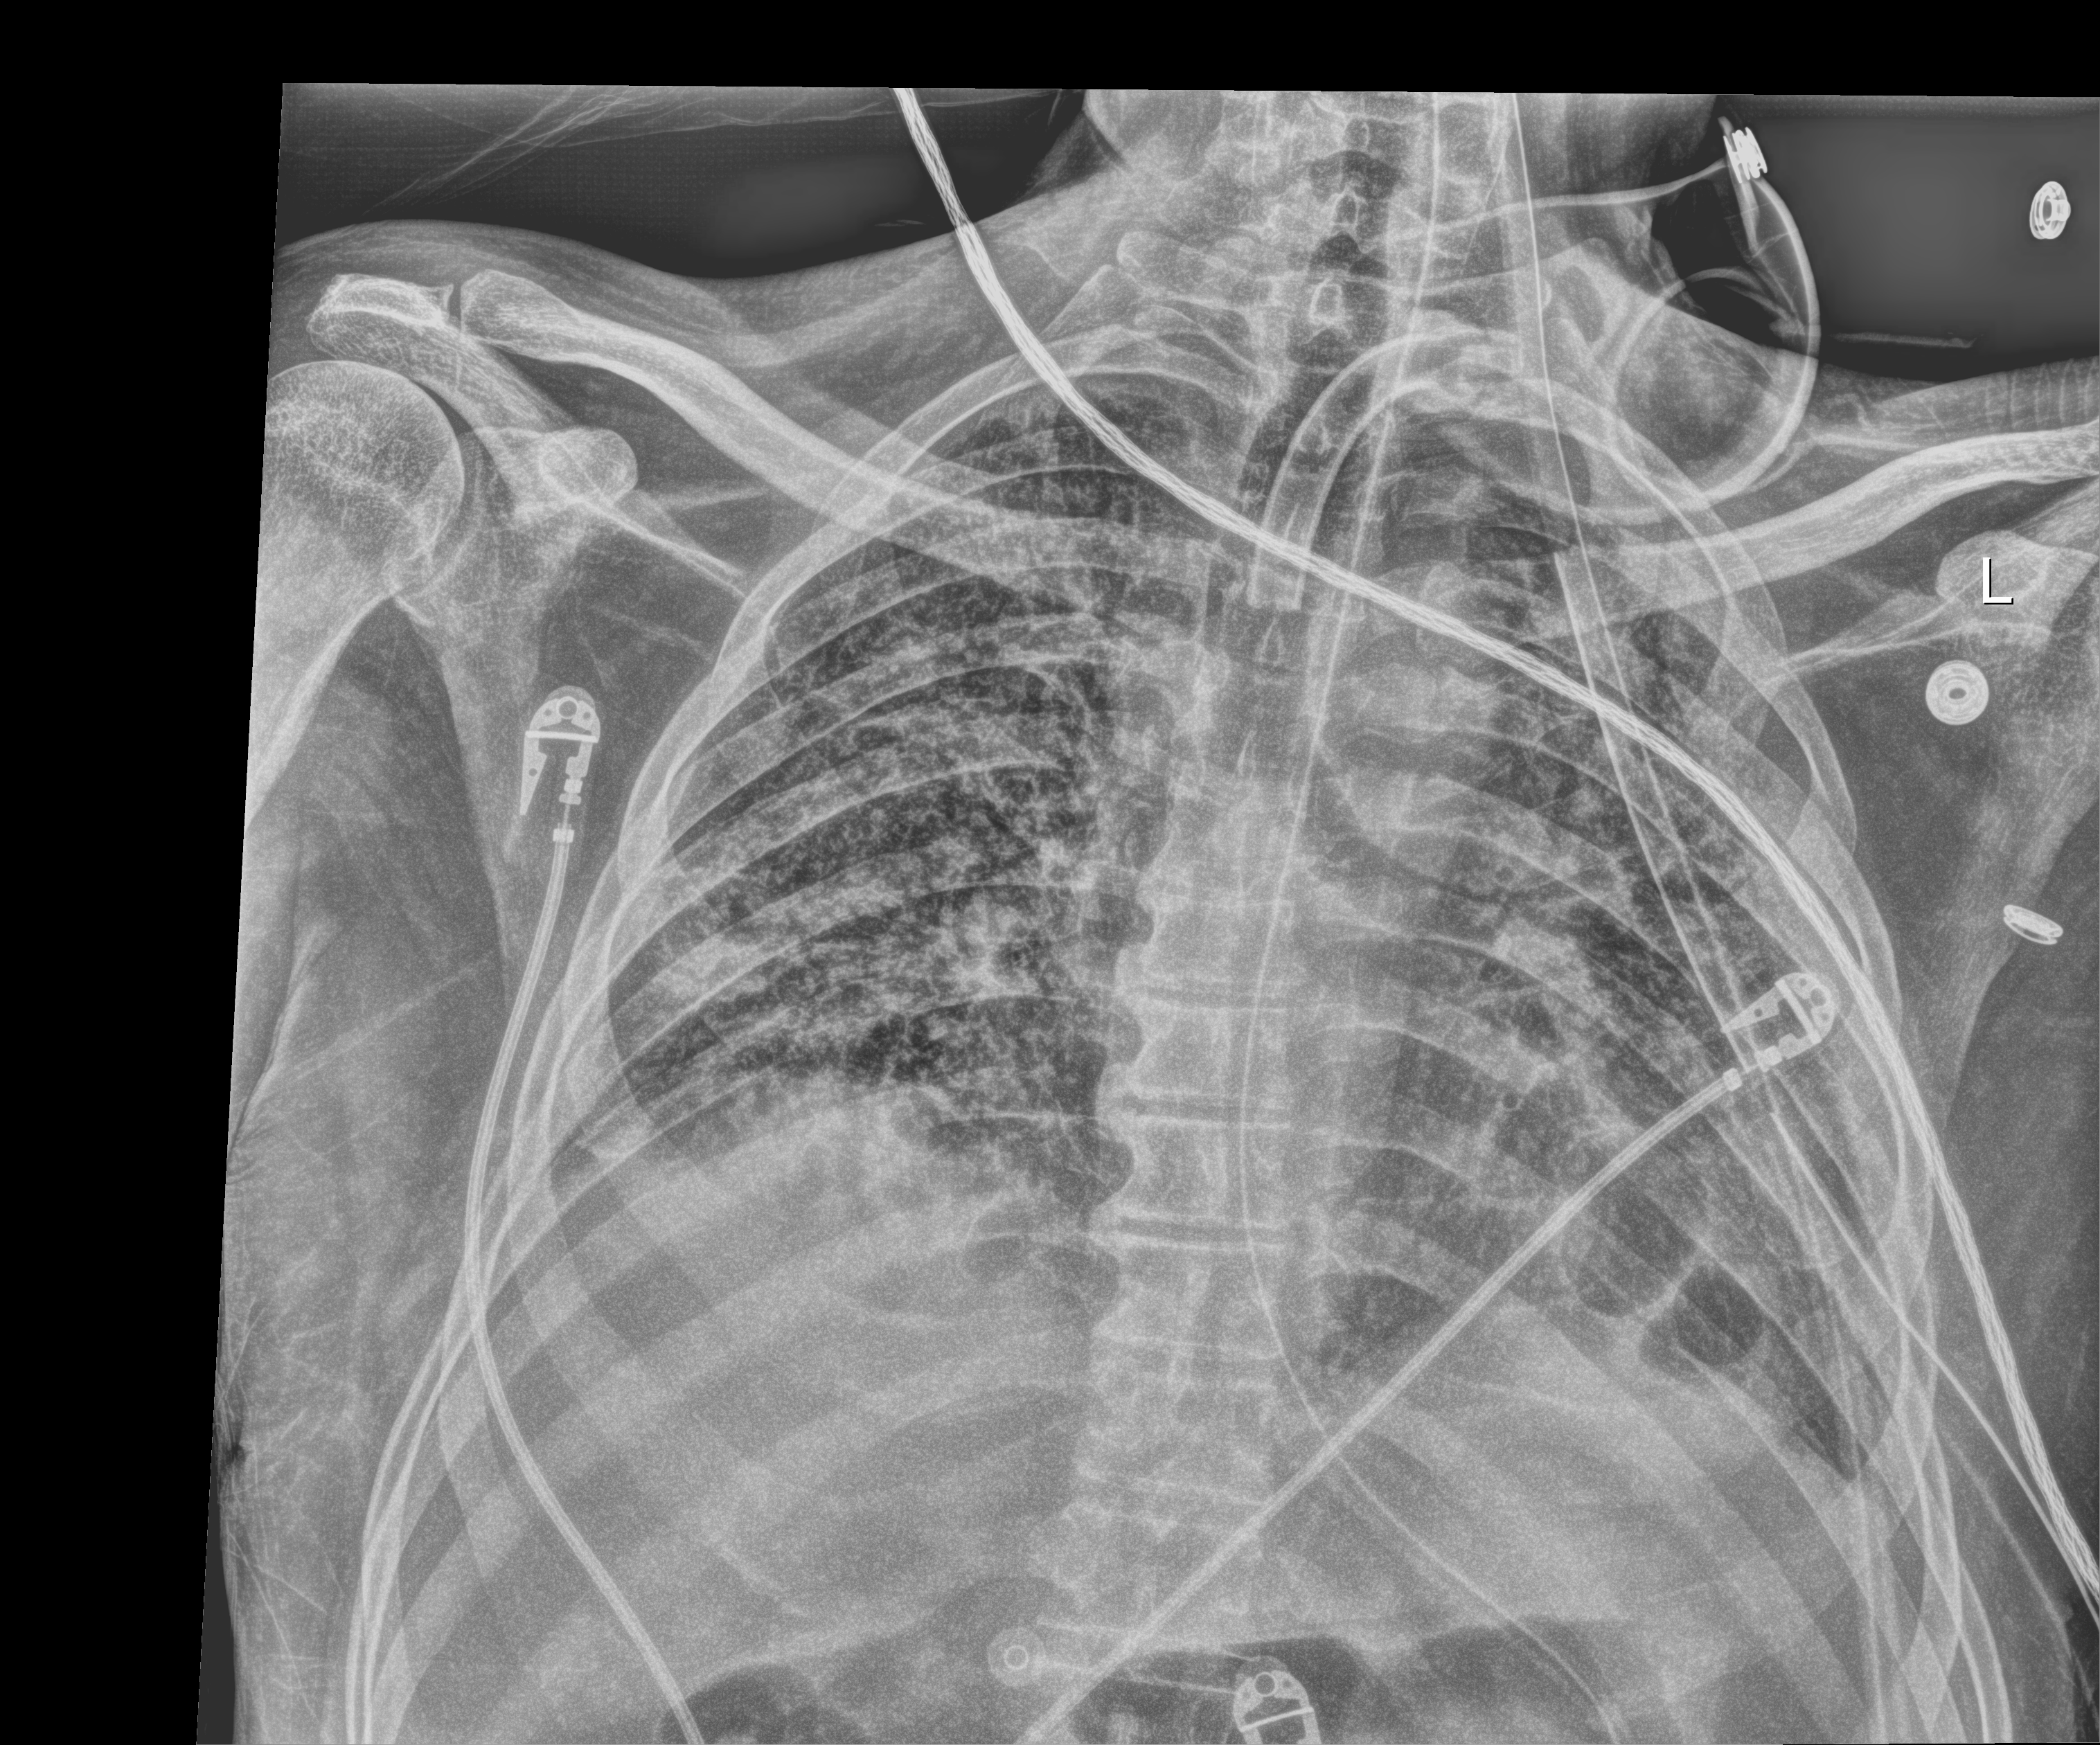
Chest X-ray (portable); anteroposterior (AP) projection. Patient hospitalised with COVID-19; male, aged 18–59 years.
Admission-level facts for this patient (not findings on this image; timing relative to this image not recorded): diabetes (admission record): no; other chronic lung disease (admission record): no.